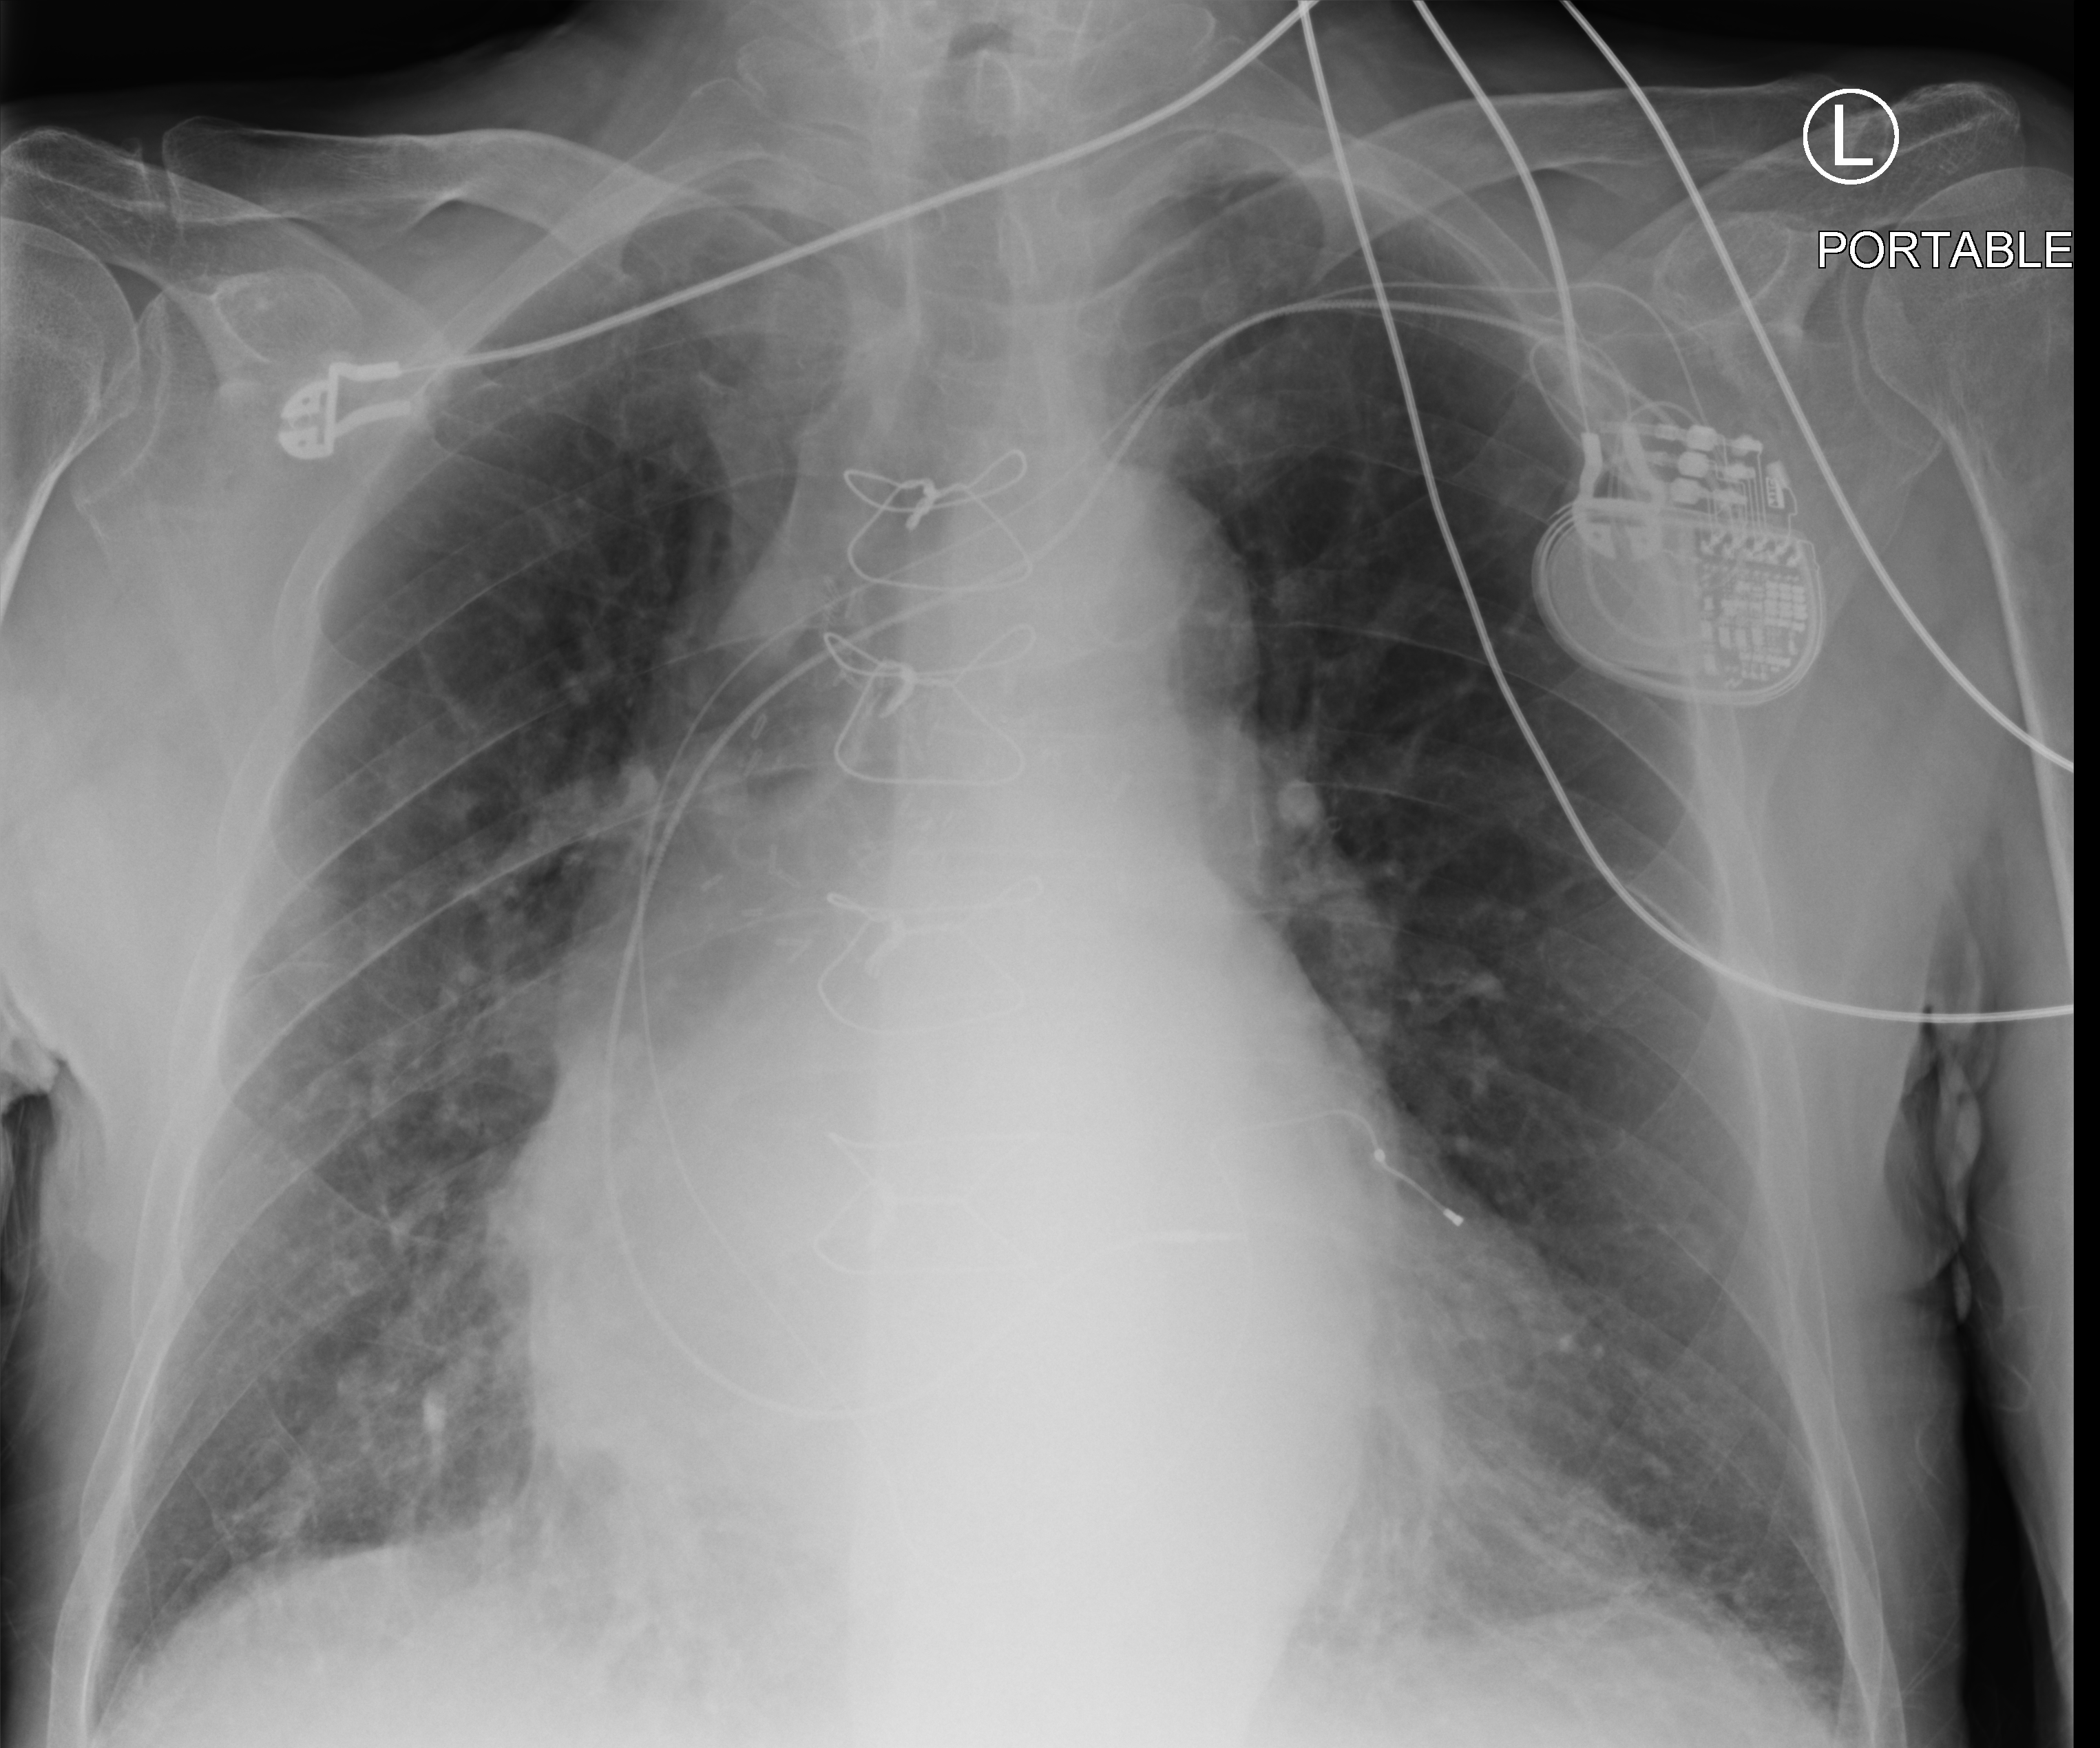
Portable chest radiograph, anteroposterior (AP) projection. Patient hospitalised with COVID-19; male, aged 75–90 years.
From the hospital-stay record, not from the radiograph (when in the stay this image was taken is not recorded): chronic kidney disease (admission record): no; mechanically ventilated during this hospital stay: no; length of hospital stay: 7 days.